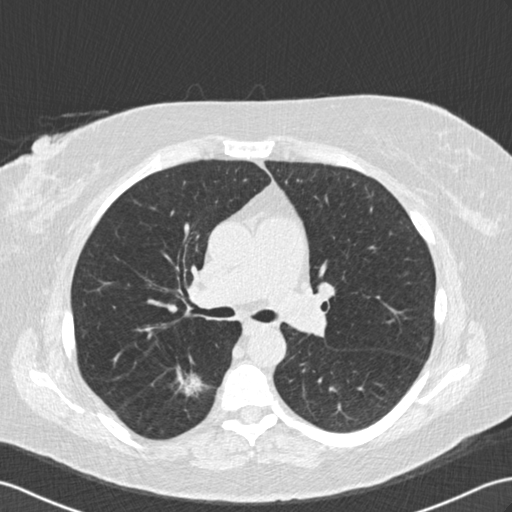
Low-dose screening chest CT, one axial slice; slice 96 of 154 in the series (ordered by position); reconstruction kernel B30f; lung window (W 1500 / L -600 HU); 2 mm slice thickness; 512 × 512 image matrix, field of view 352 × 352 mm.
Structures marked on this image (expert manual segmentation):
- lesion 1 (tumor, lower lobe of right lung): bounding box <176,366,206,397> (left, top, right, bottom; pixels)